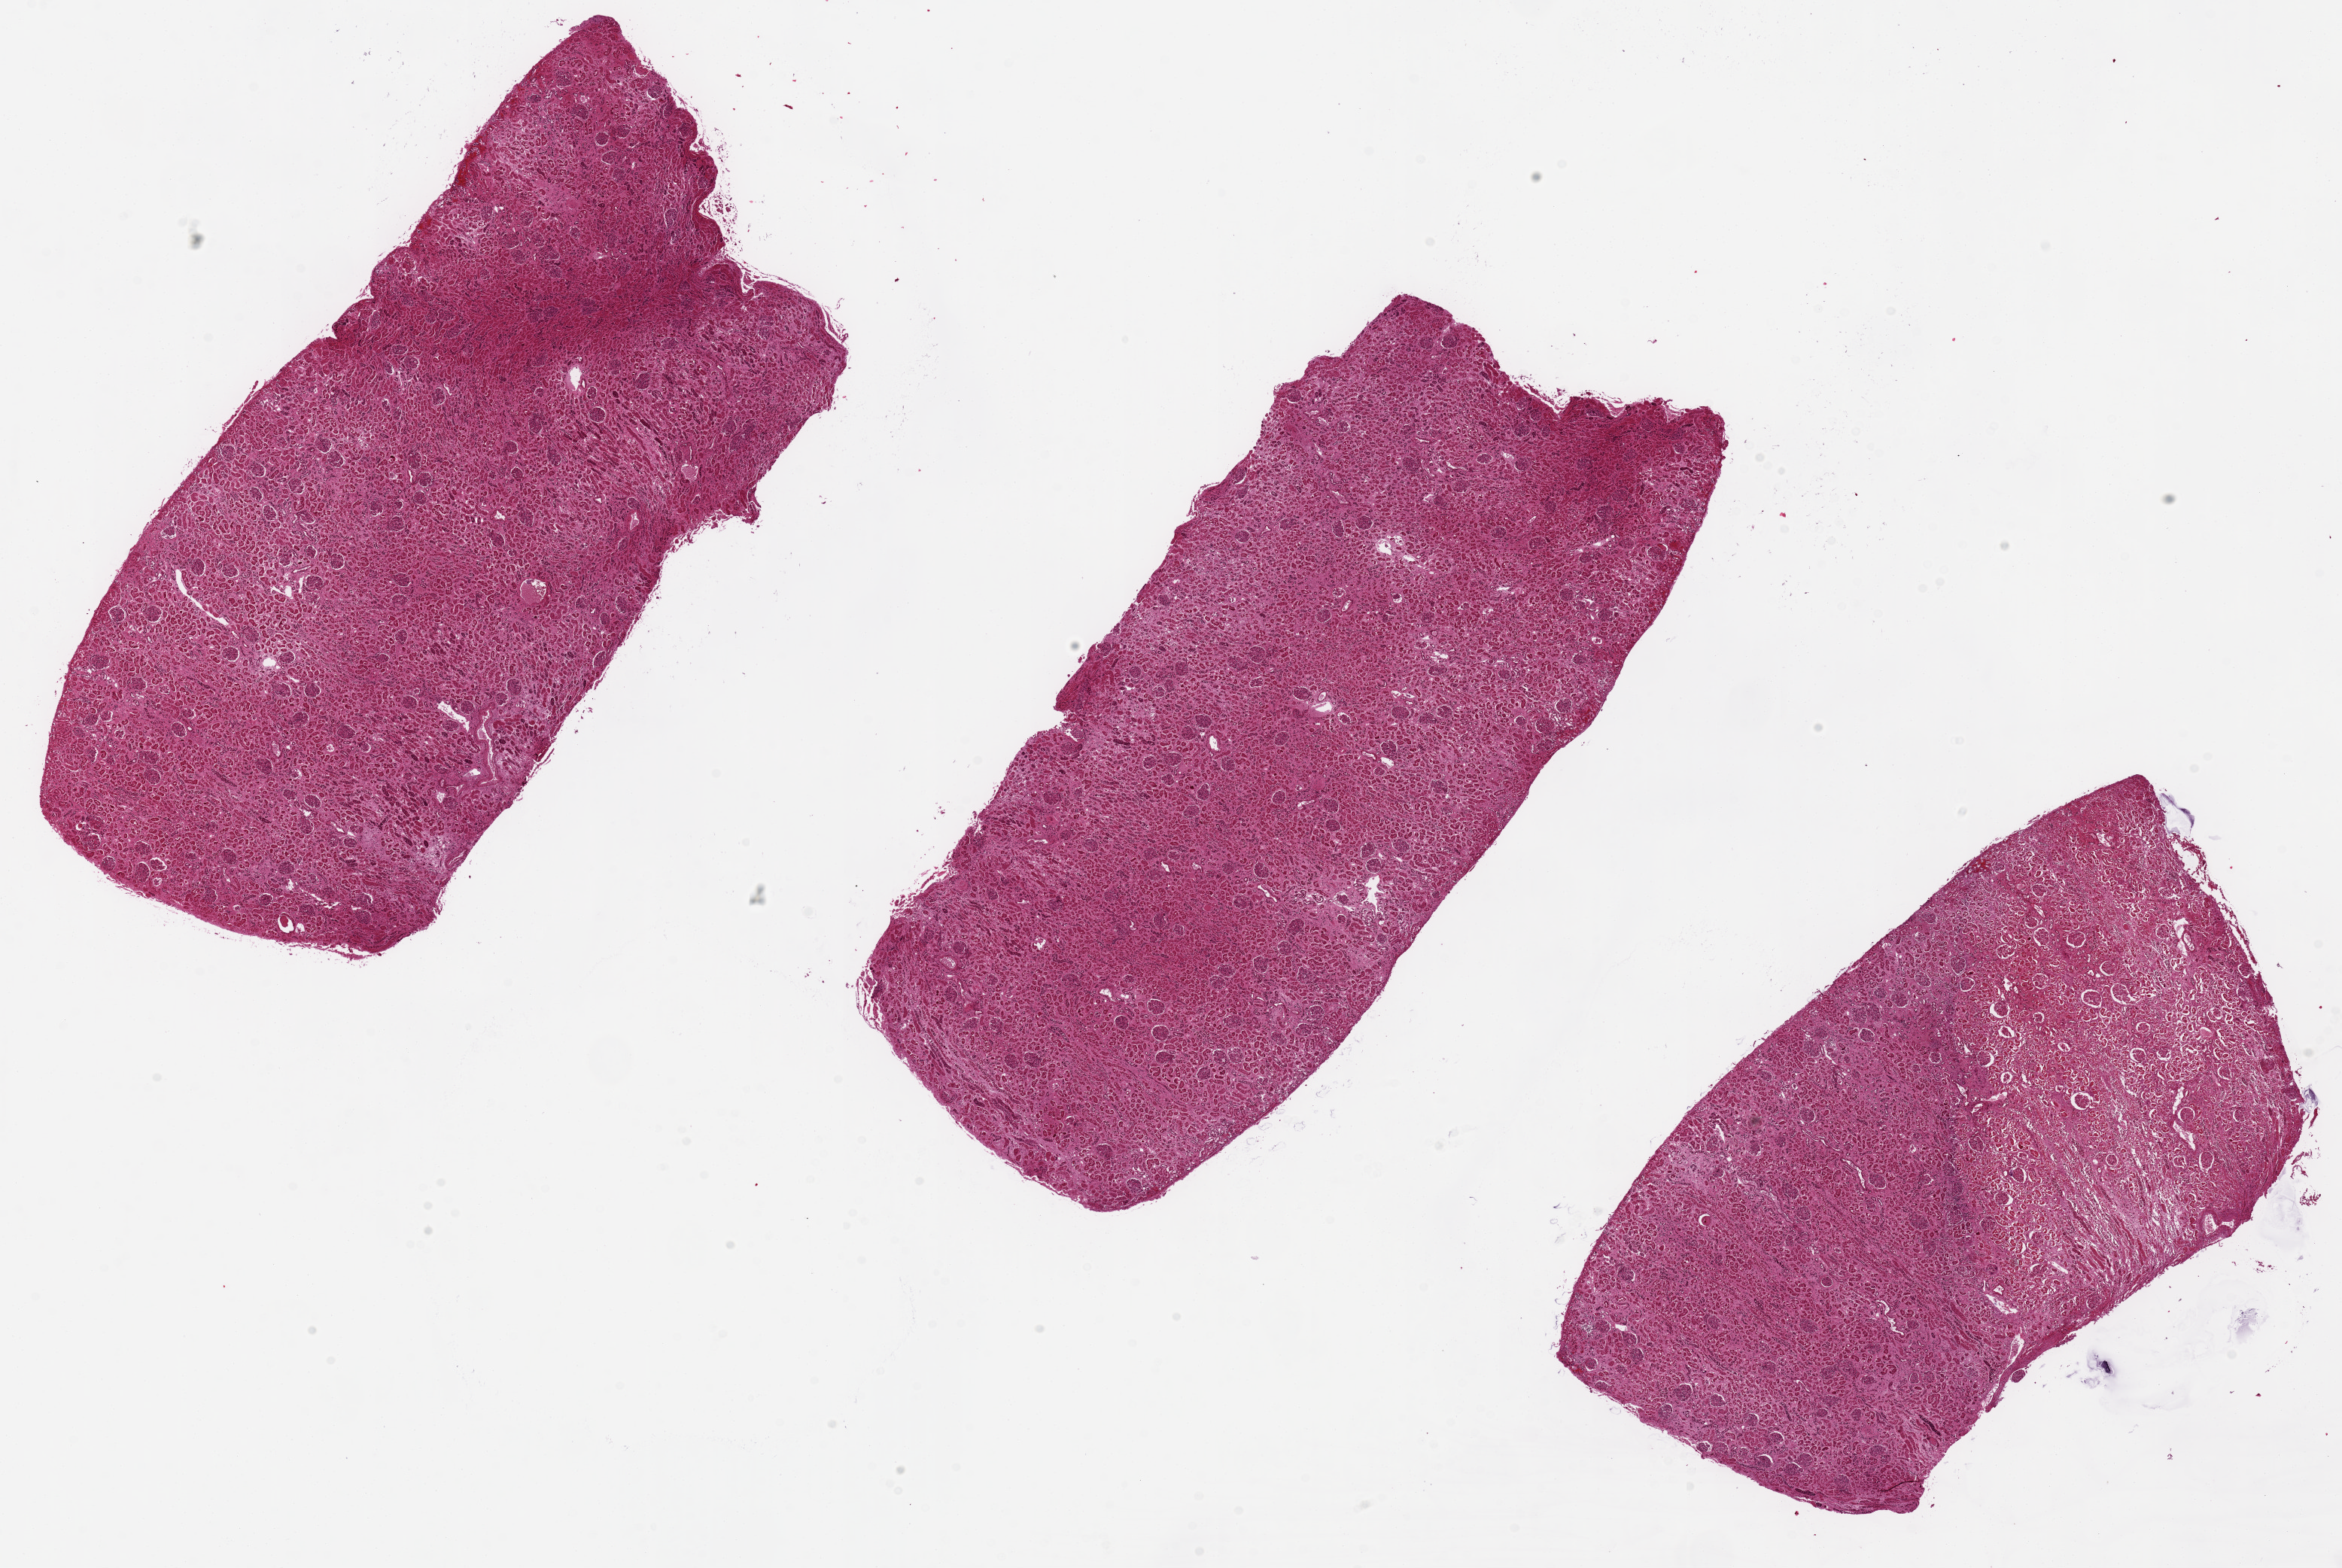
Whole-slide image, haematoxylin and eosin stain — shown as a low-resolution overview of the whole scanned area (about 24.6 x 16.5 mm, slide scanned at 20x); PAXgene-fixed, paraffin-embedded tissue; sampled site (target tissue): renal cortex; tissue donor sample.
Pathologist's review note for this sample: Tubules most autolyzed. No sign of.